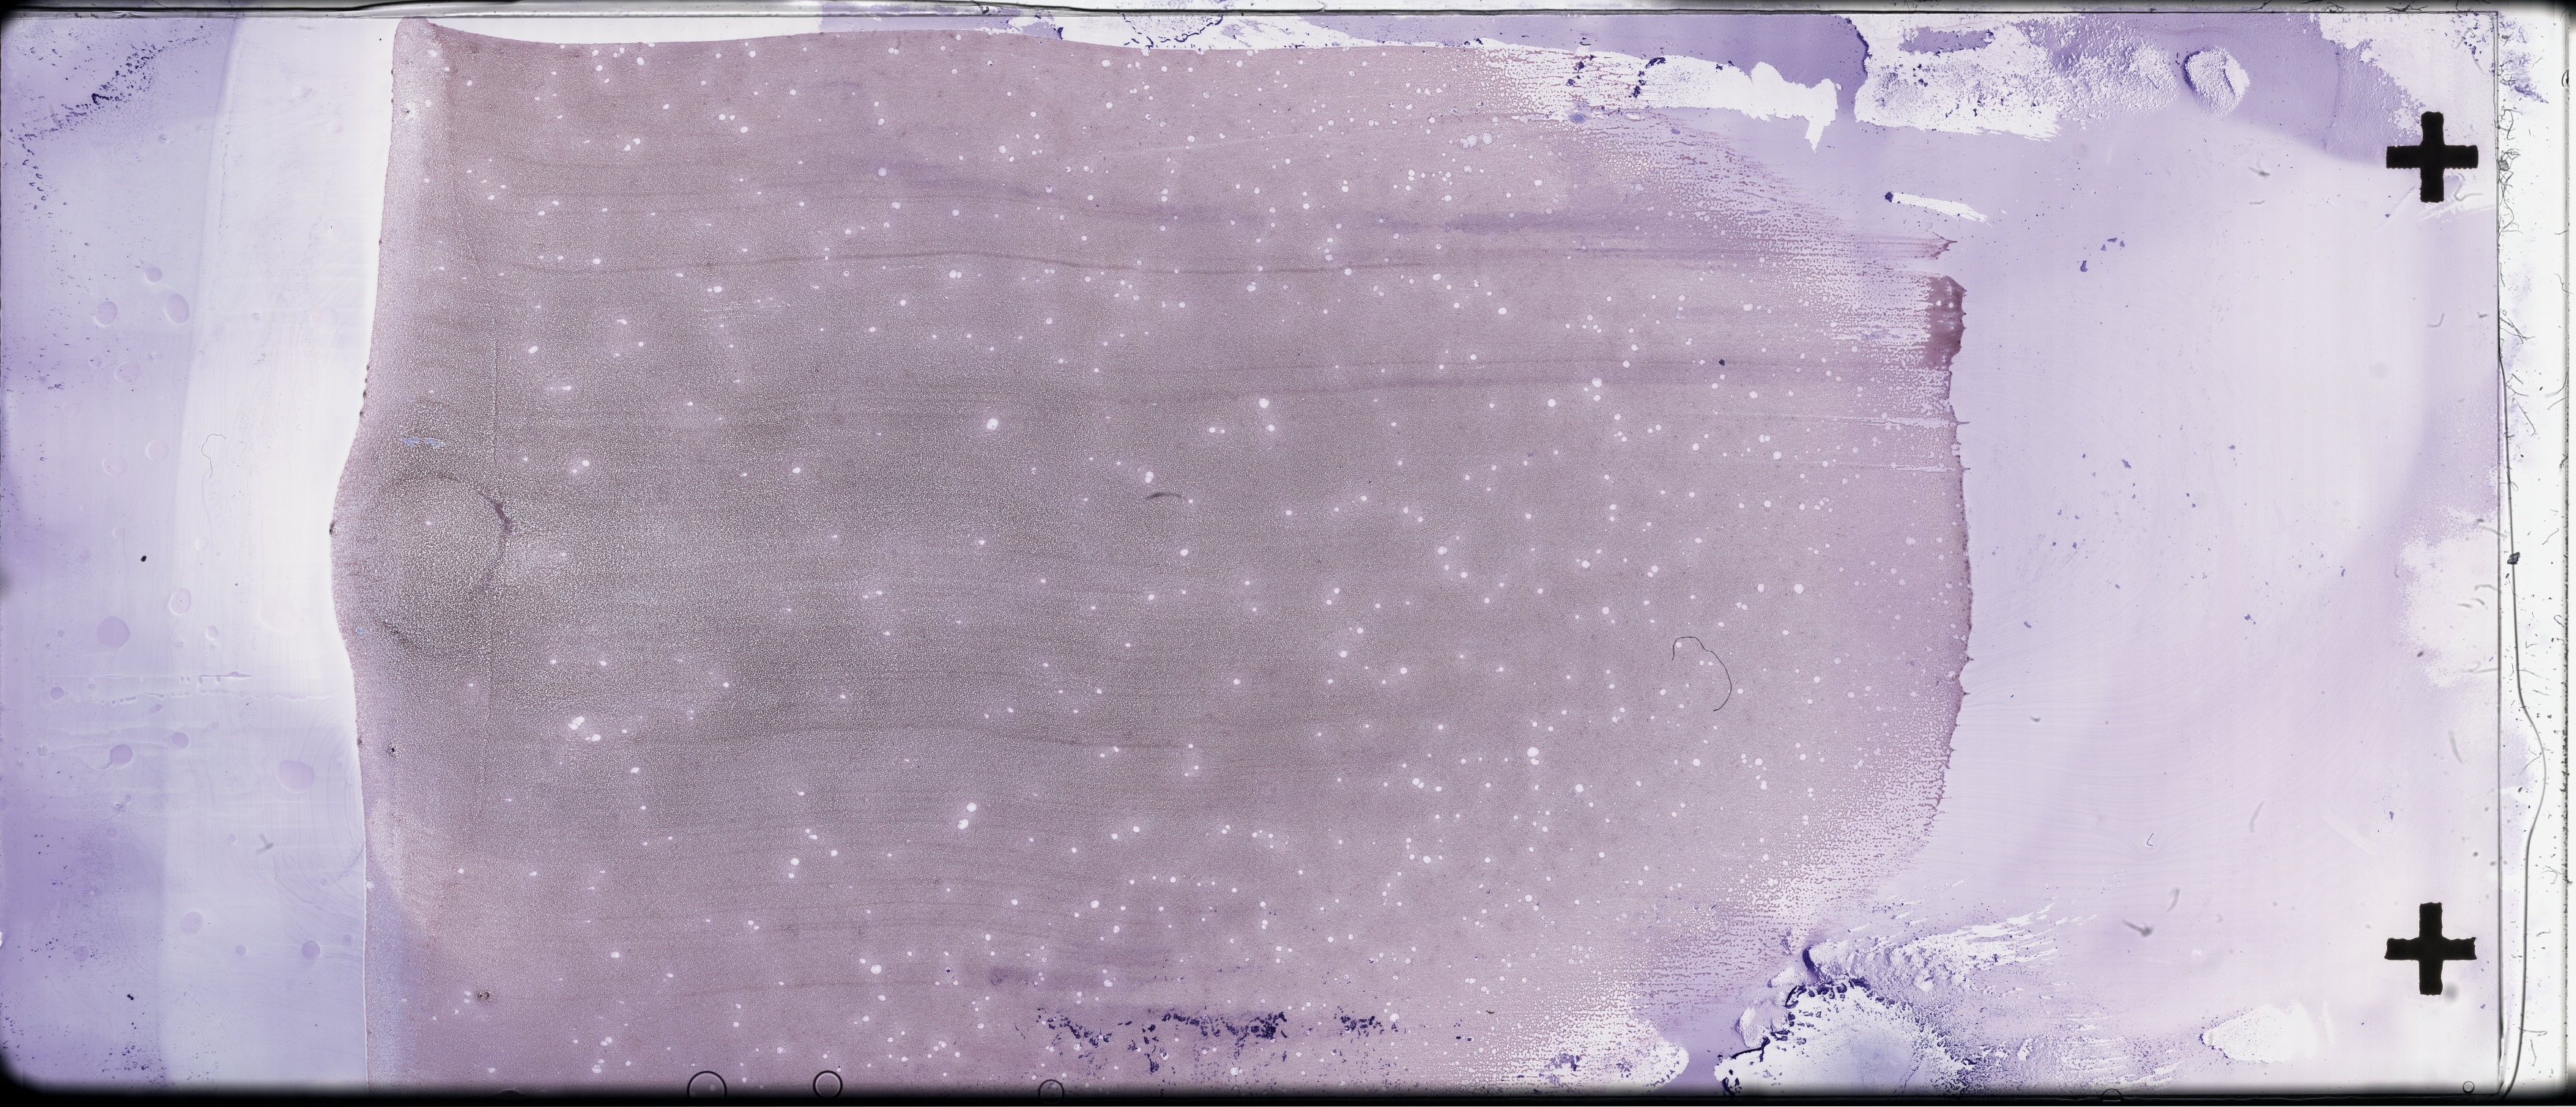
Whole-slide image of a whole blood smear, Wright–Giemsa stain — whole scanned area (about 56.8 x 24.4 mm) shown as a low-resolution overview; EDTA-anticoagulated smear; specimen time point: collected on treatment. Patient sex: female.
From a patient with: Plasma Cell Myeloma.